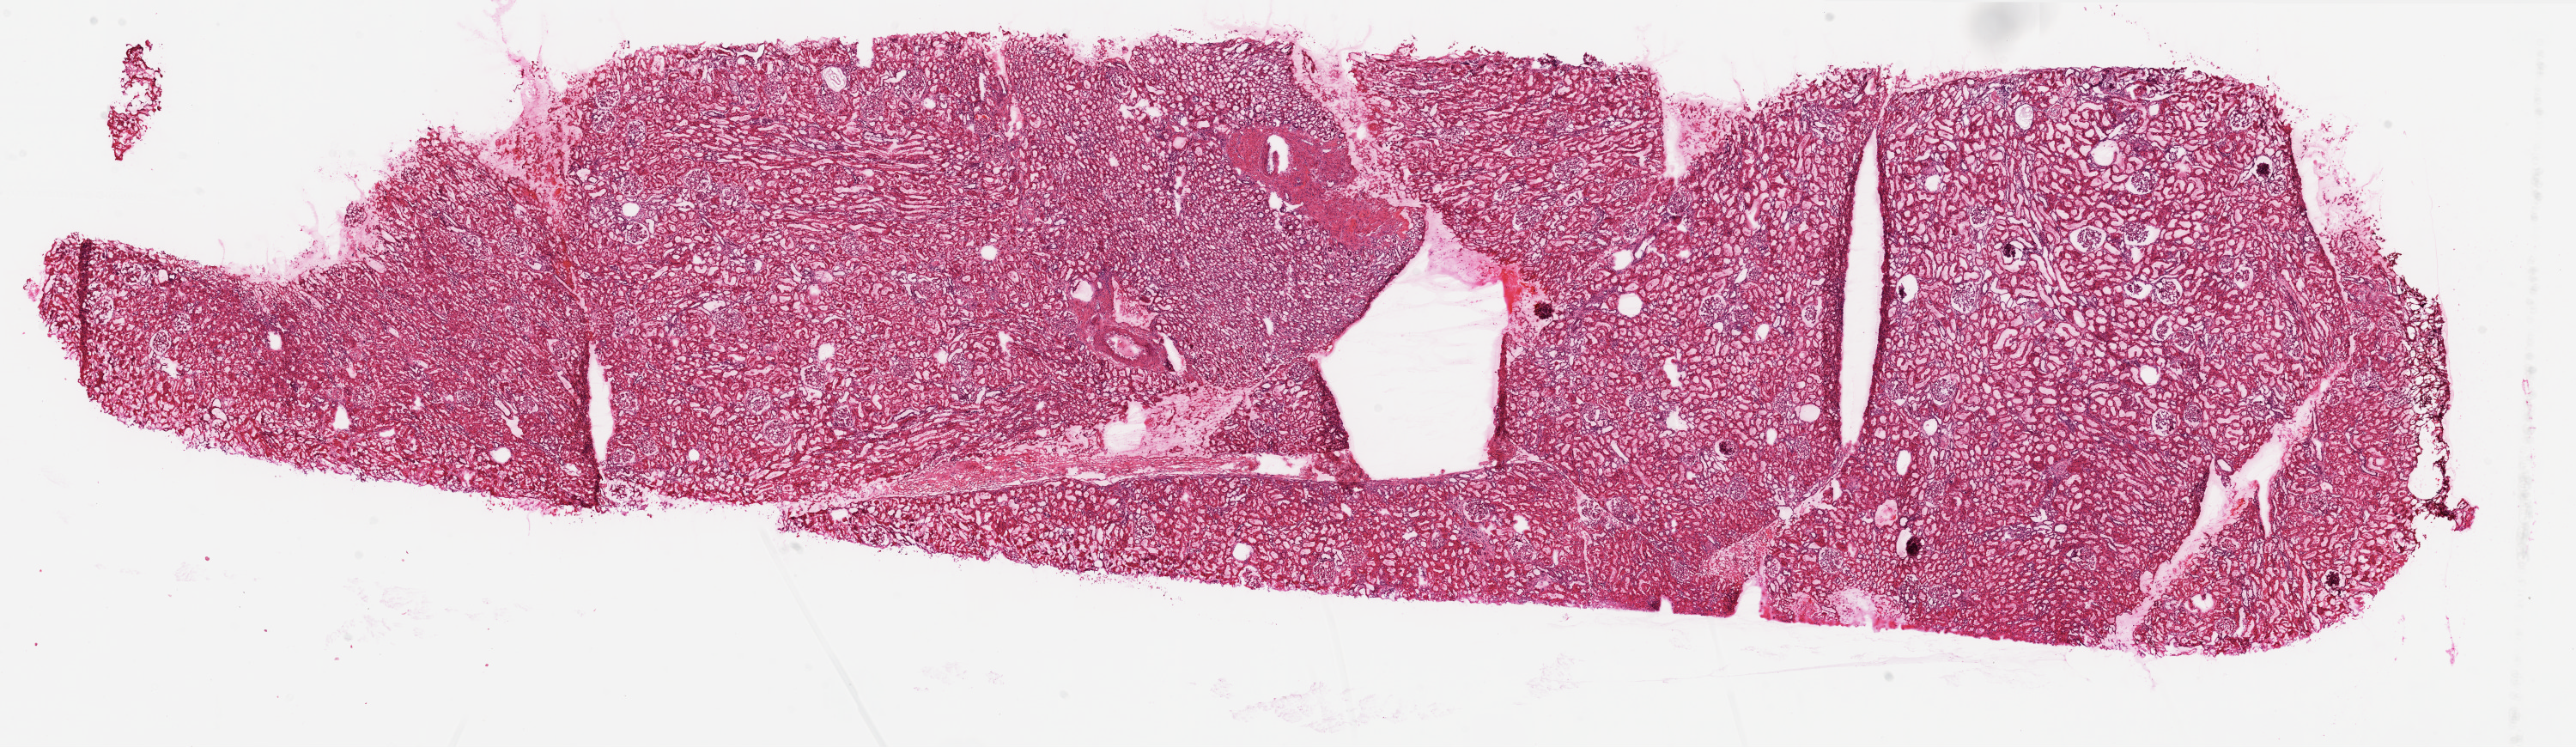
Digitized H&E-stained tissue section (whole slide) — whole scanned area (about 24.1 x 7.0 mm, acquisition: 20x scan) shown as a low-resolution overview; frozen section from the top of the tissue portion; sample: solid tissue normal (non-tumour tissue), kidney. Patient: male, age at initial diagnosis 42 years.
• this section: solid tissue normal sample (biorepository sample class)
• patient diagnosis: Clear cell adenocarcinoma, NOS